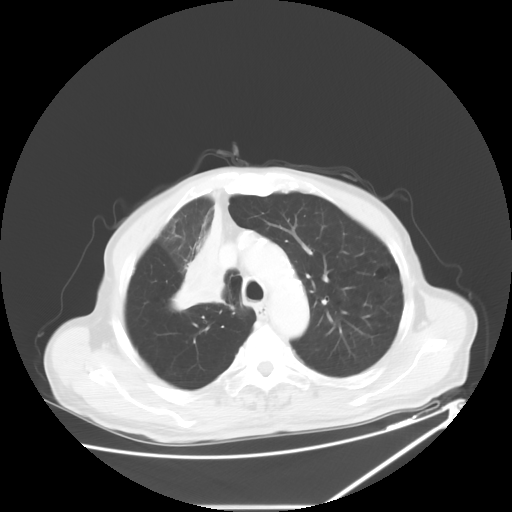
Chest CT, one axial slice. Position 46 of 60 along the scan axis. Lung window (W 1500 / L -600 HU). 5 mm slice thickness. 512 × 512 image matrix, field of view 410 × 410 mm. Patient: male, 73 years. From the clinical record (not read from this slice): clinical TNM (as recorded): T2a N1 M0.
Outlined on this slice (rectangle marked by the reading radiologist):
- lung tumour (recorded histology: squamous cell carcinoma): bounding box [x1, y1, x2, y2] px = [175, 194, 224, 324]